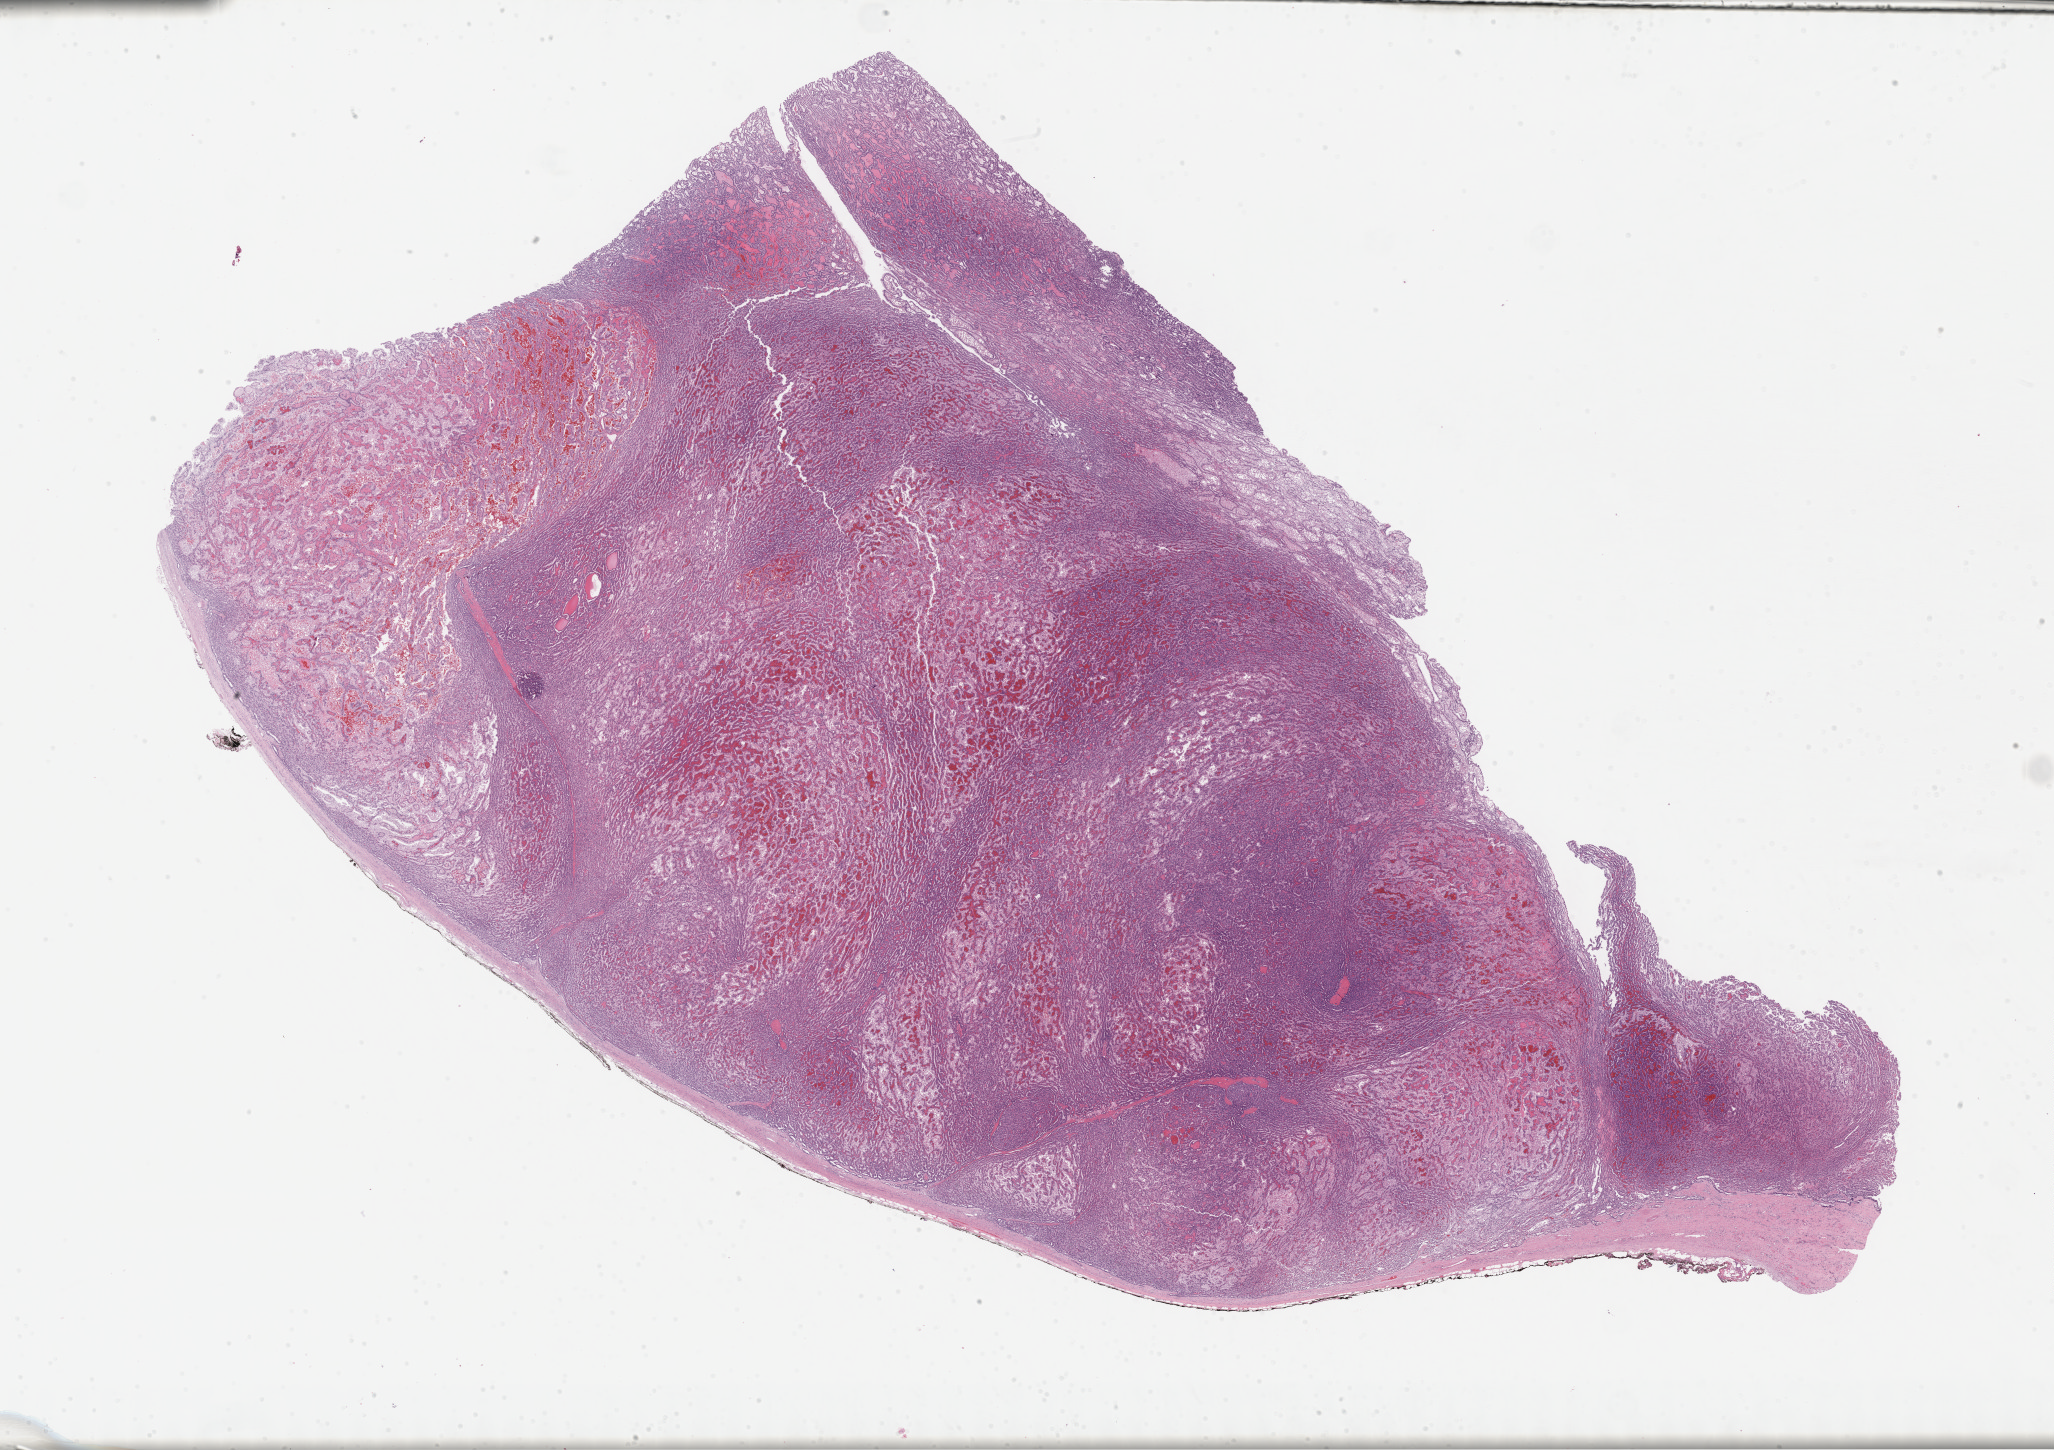
Hematoxylin and eosin (H&E) stained whole-slide image, a low-resolution overview of the entire scanned area, about 33.2 x 23.5 mm (slide scanned at 40x). FFPE section. Sample: primary tumour, kidney. Male patient; age at initial diagnosis 65 years.
* laterality: right
* pathologic diagnosis: Papillary adenocarcinoma, NOS
* AJCC pathologic stage: I (7th edition)